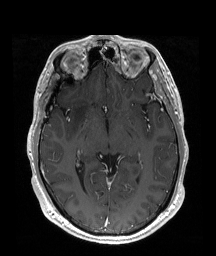
Brain MRI from a brain-tumour surgery series, one axial slice; slice 110 of 192 in the series (ordered by position); T1-weighted post-contrast; 216 × 256 image matrix. Case-level facts recorded for this patient, not image findings: histopathology: Astrocytoma; WHO grade: 2; IDH mutation: yes.
Structures marked on this image (outlined manually by an expert reader):
- tumour: bounding box <69,95,91,135> (left, top, right, bottom; pixels)